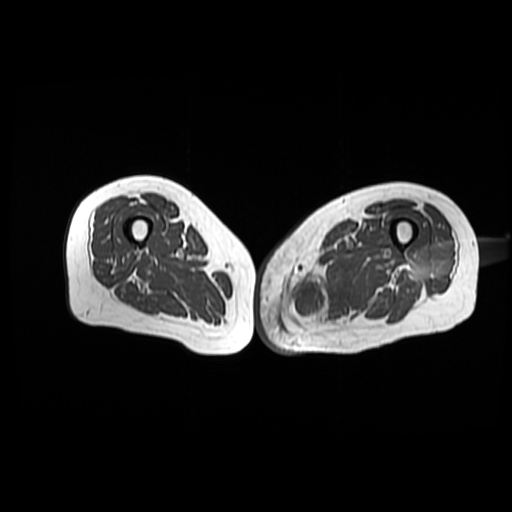
MRI of an extremity soft-tissue mass, one axial slice; slice 39 of 42 in the series (ordered by position); 6 mm slice thickness; 512 × 512 image matrix. Female patient. Case-level facts recorded for this patient, not image findings: histological type: pleomorphic leiomyosarcoma; grade: high; site of the primary tumour: left thigh.
Structures marked on this image (outlined manually by an expert reader):
- gross tumour volume including surrounding oedema: bounding box [x1, y1, x2, y2] px = [288, 260, 351, 330]